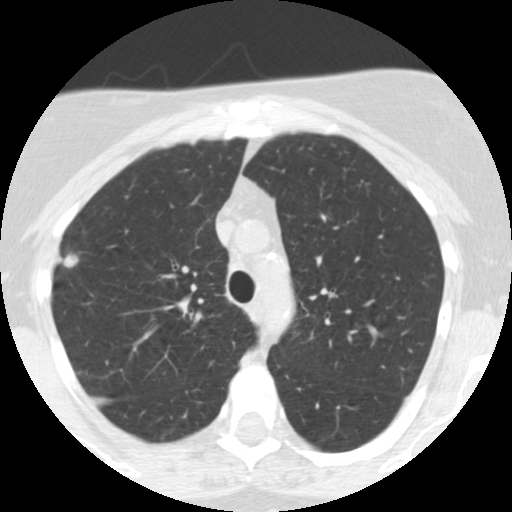
Low-dose screening chest CT, one axial slice; slice 183 of 248 in the series (ordered by position); reconstruction kernel STANDARD; 120 kVp; lung window (W 1500 / L -600 HU); 512 × 512 image matrix, field of view 287 × 287 mm.
Outlined on this slice (expert manual segmentation):
- lesion 1 (tumor, upper lobe of right lung): bounding box (x1, y1, x2, y2) in pixels: (63, 254, 79, 268)